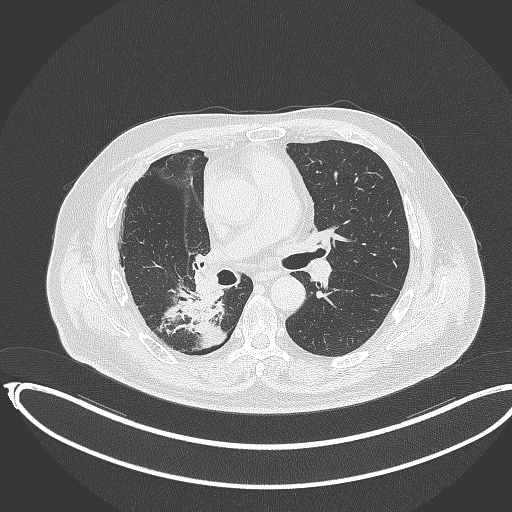
Chest CT, one axial slice; position 194 of 403 along the scan axis; reconstruction kernel B70f; 120 kVp; lung window (W 1500 / L -600 HU); 1 mm slice thickness; 512 × 512 image matrix, field of view 436 × 436 mm. Patient: male, 68 years. From the clinical record (not read from this slice): clinical TNM (as recorded): T2a N0 M0.
Annotated regions visible in this slice (rectangle marked by the reading radiologist):
- lung tumour (recorded histology: adenocarcinoma): bounding box <155,285,234,352> (left, top, right, bottom; pixels)